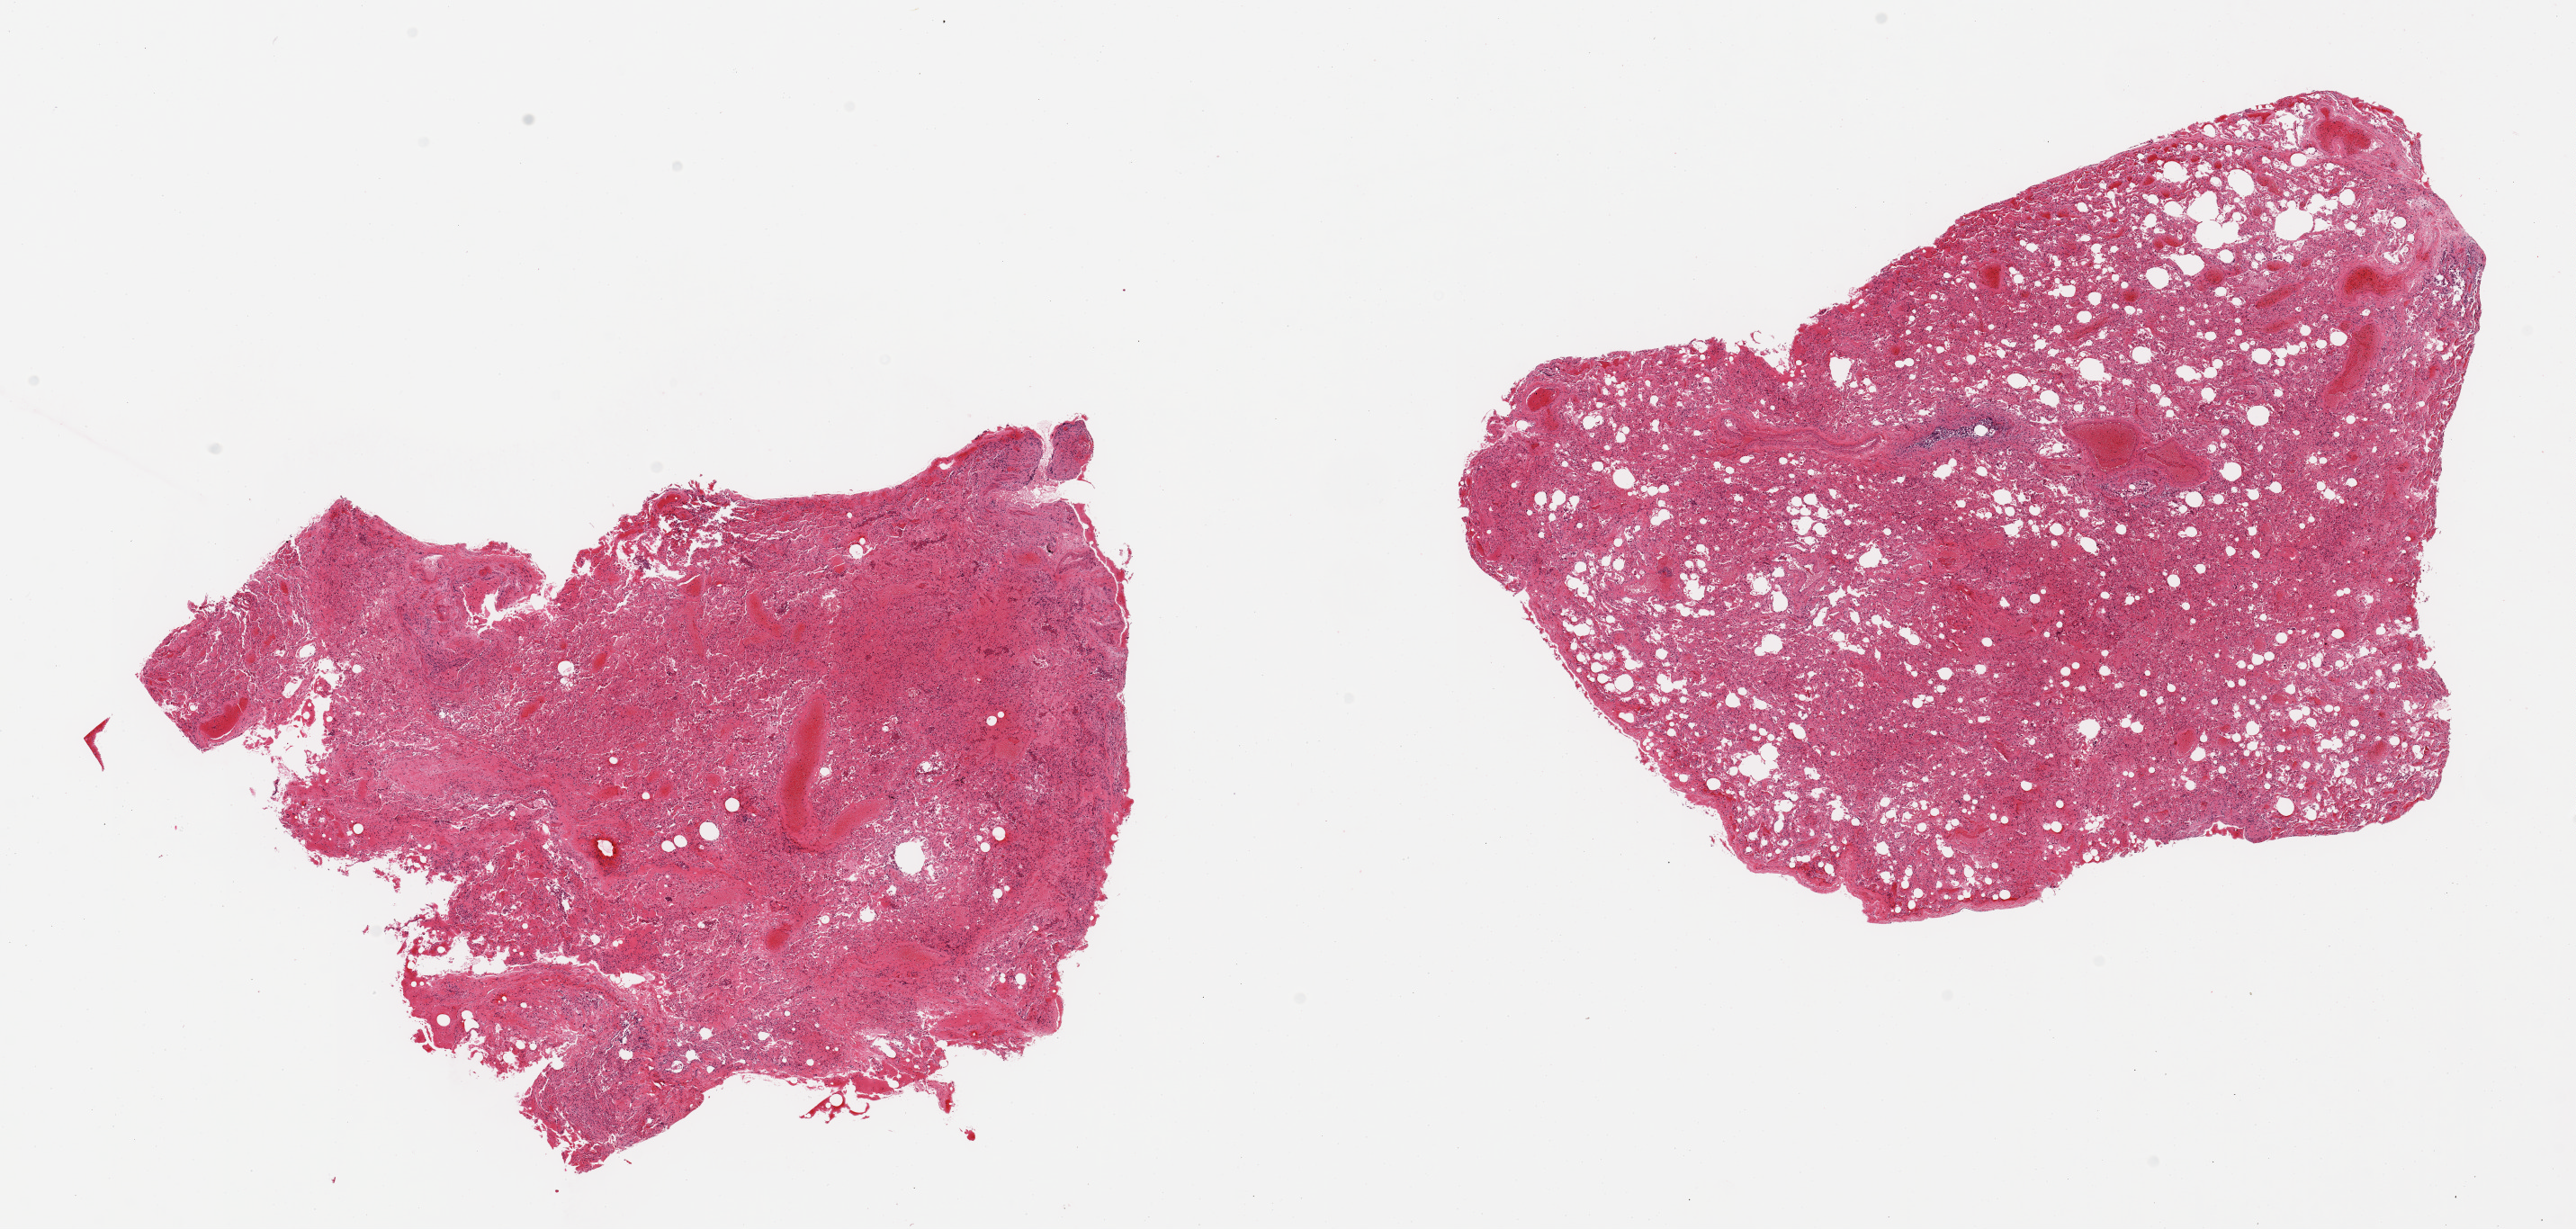
Whole-slide image, hematoxylin and eosin (H&E) stain, a low-resolution overview of the entire scanned area, about 22.6 x 10.8 mm. PAXgene-fixed paraffin-embedded (PFPE) section. Target tissue: lung. Donor tissue sample. Donor sex: female.
• pathologist's review note for this sample: 2 pieces; atelectasis, hemorrhage, fibrosis